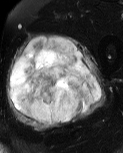
MRI of an extremity soft-tissue mass, one axial slice. Position 29 of 60 along the scan axis. T2-weighted fat-saturated. MR volume resampled by the dataset authors to the PET/CT grid (not the native acquisition matrix). 3.27 mm slice thickness. 123 × 153 image matrix, field of view 120 × 149 mm. Male patient. Case-level facts recorded for this patient, not image findings: histological type: pleiomorphic liposarcoma; grade: high; site of the primary tumour: left thigh.
Annotated regions visible in this slice (expert contour drawn on MRI and transferred to this co-registered scan by the dataset authors):
- gross tumour volume including surrounding oedema: box from (x=6, y=33) to (x=105, y=131) px
- gross tumour volume (mass): (x=9, y=36)–(x=101, y=124)